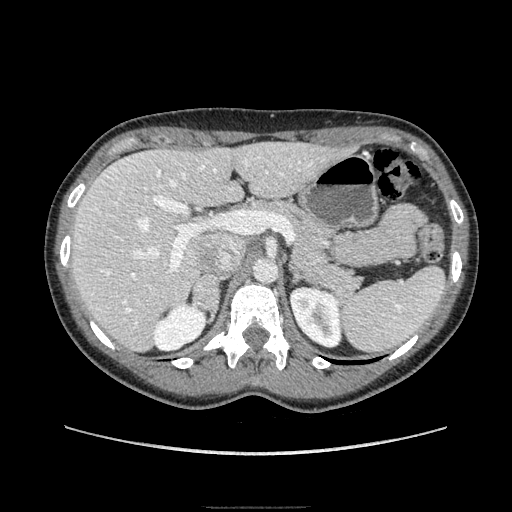
Contrast-enhanced abdominal CT, one axial slice. Soft-tissue window (W 400 / L 40 HU). 1.25 mm slice thickness. 512 × 512 image matrix, field of view 380 × 380 mm. Female patient. From the clinical record (not read from this slice): diagnosis: adrenocortical carcinoma; tumour side: right adrenal; tumour size at pathology: 3 cm; Ki-67 index: 4 %.
Structures marked on this image (semi-automatic segmentation, software-assisted and operator-edited):
- mass: box from (x=195, y=276) to (x=218, y=321) px